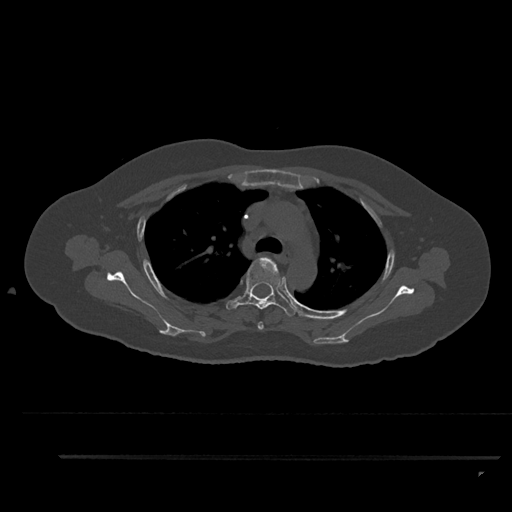
CT including the spine, one axial slice; slice 651 of 797 in the series (ordered by position); bone window (W 1800 / L 400 HU); 512 × 512 image matrix. Patient: female, 44 years. Case-level facts recorded for this patient, not image findings: primary cancer: renal; vertebrae with lytic lesions (as recorded): L1.
Annotated regions visible in this slice (semi-automatic segmentation, software-assisted and operator-edited):
- T3 vertebra: bounding box <258,321,264,330> (left, top, right, bottom; pixels)
- T4 vertebra: <226,257,297,317>